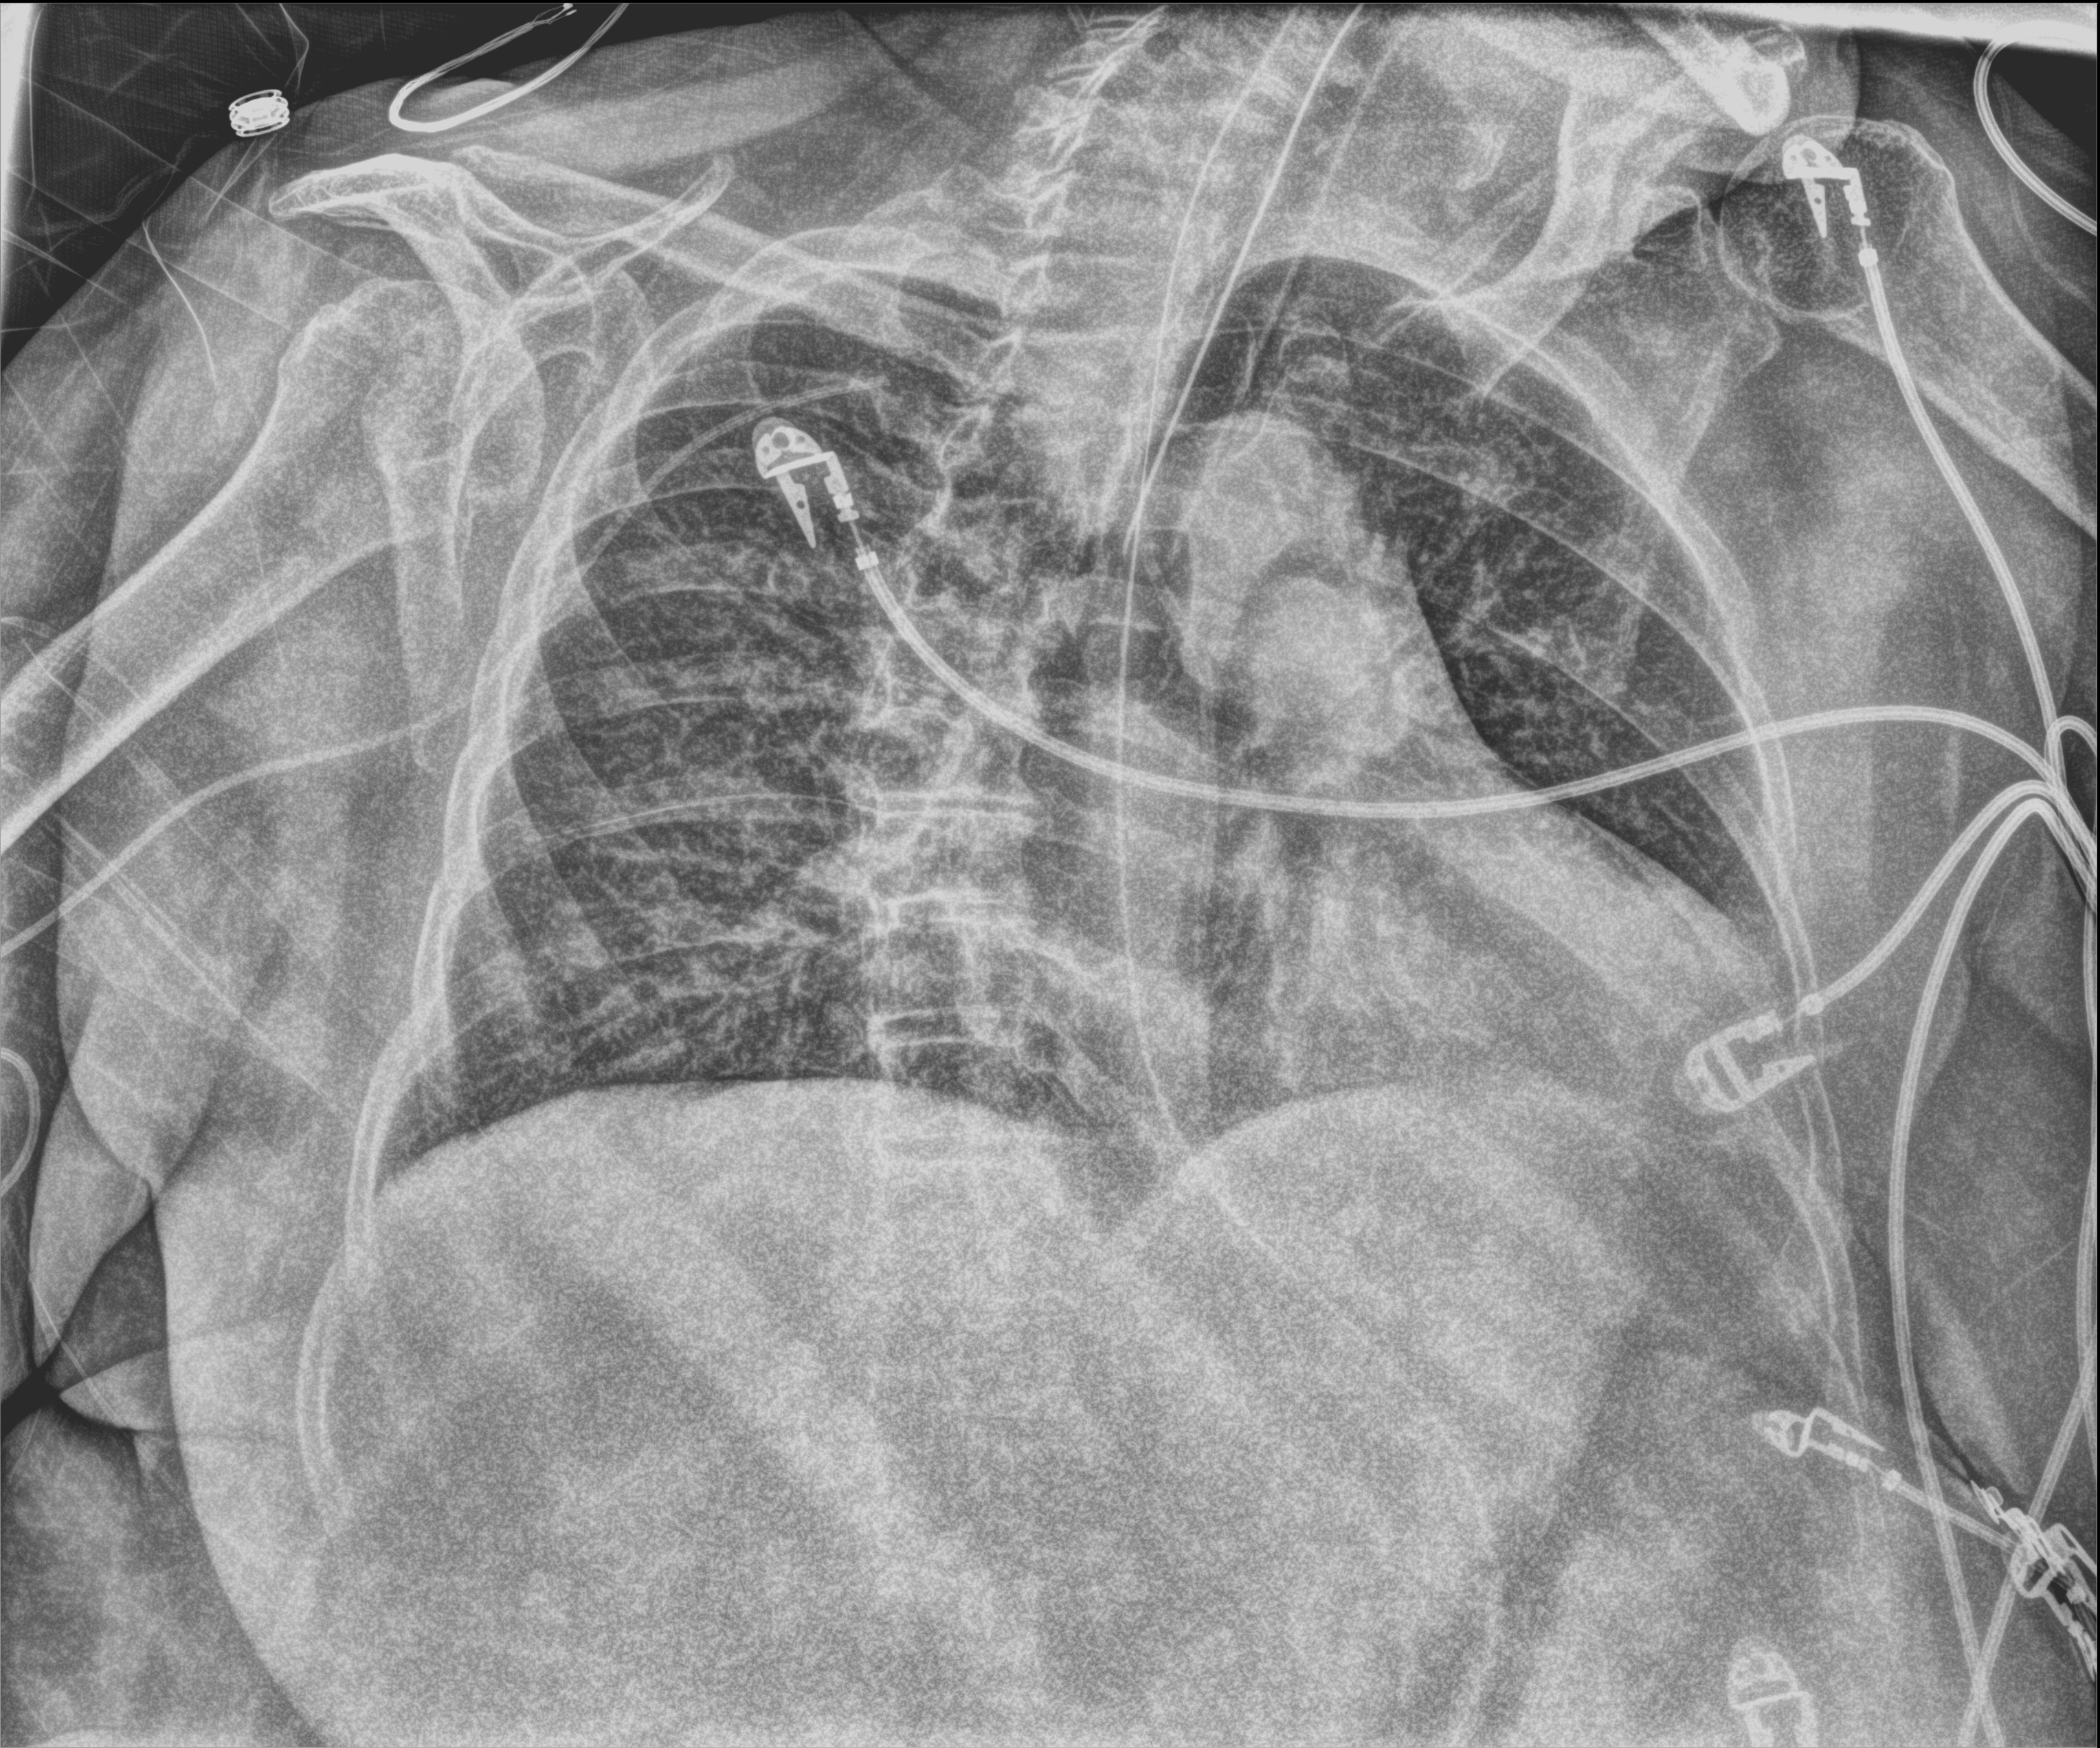
Portable chest radiograph; anteroposterior (AP) projection. Patient hospitalised with COVID-19; female, aged 75–90 years.
From the hospital-stay record, not from the radiograph (when in the stay this image was taken is not recorded): mechanically ventilated during this hospital stay: yes; admitted to intensive care during this hospital stay: yes.